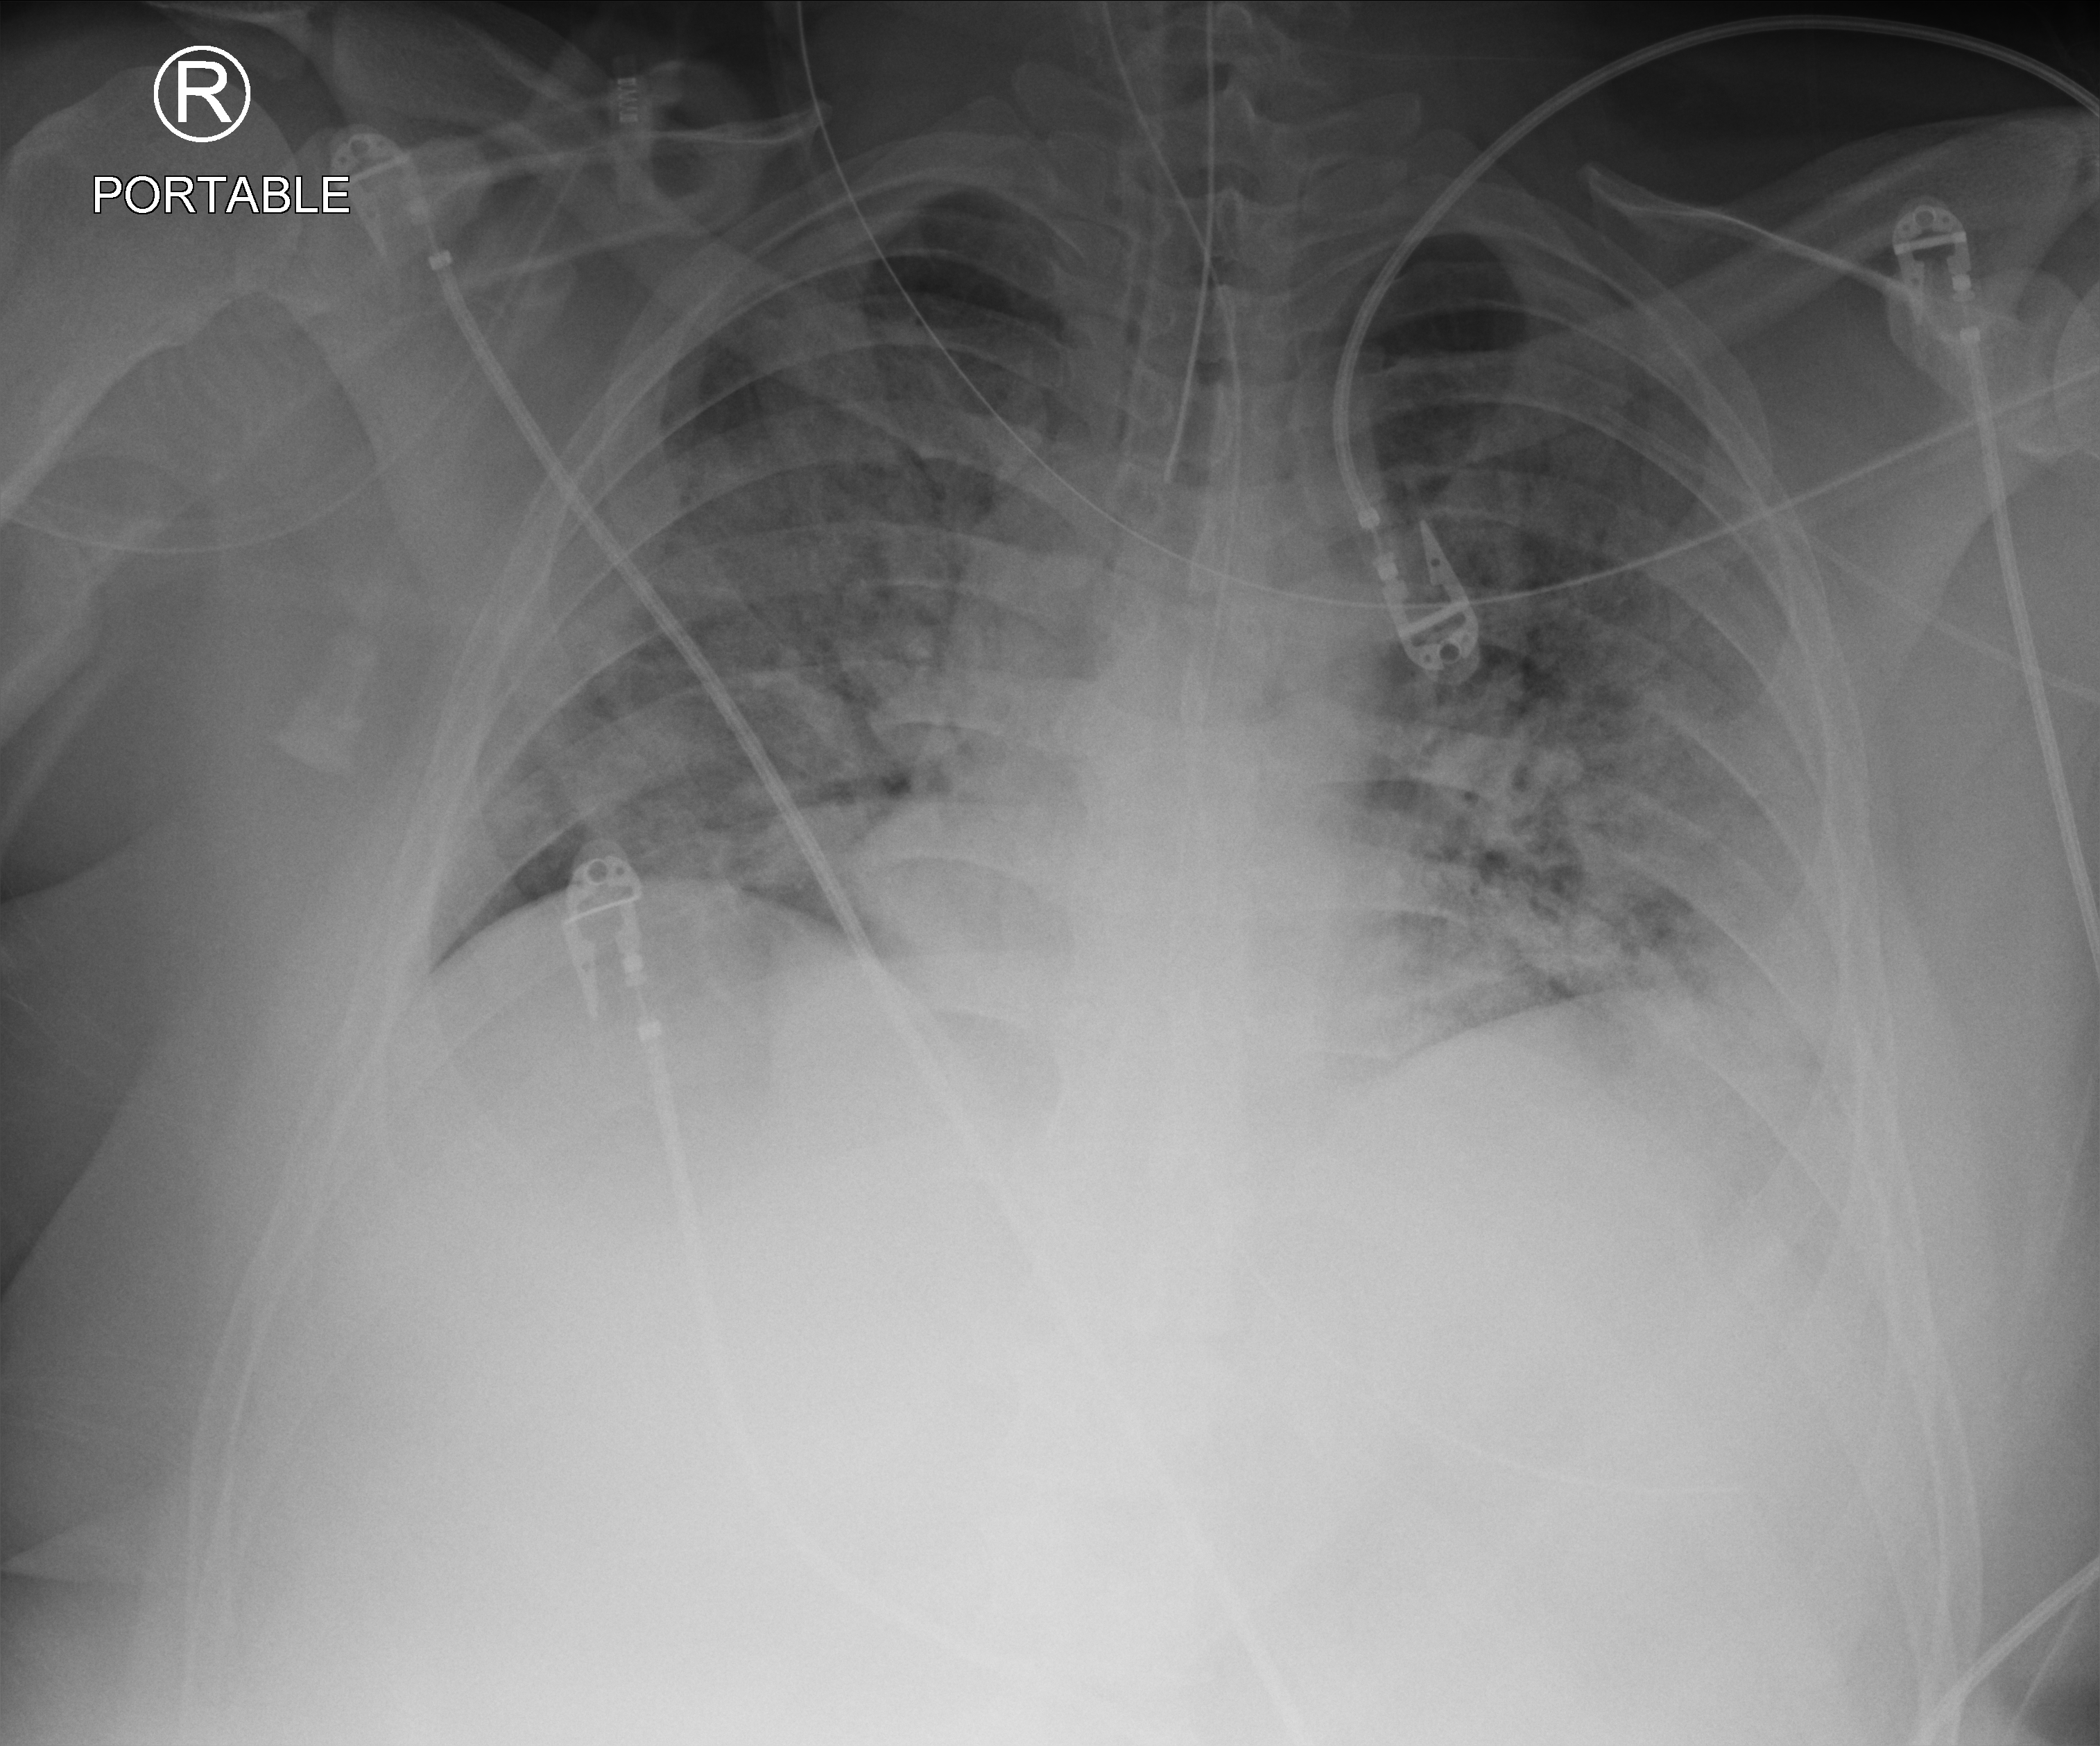
Portable chest radiograph; anteroposterior (AP) projection. Adult patient hospitalised with COVID-19, age 18–59 years.
Admission-level facts for this patient (not findings on this image; timing relative to this image not recorded): admitted to intensive care during this hospital stay: yes; other chronic lung disease (admission record): no; mechanically ventilated during this hospital stay: yes.